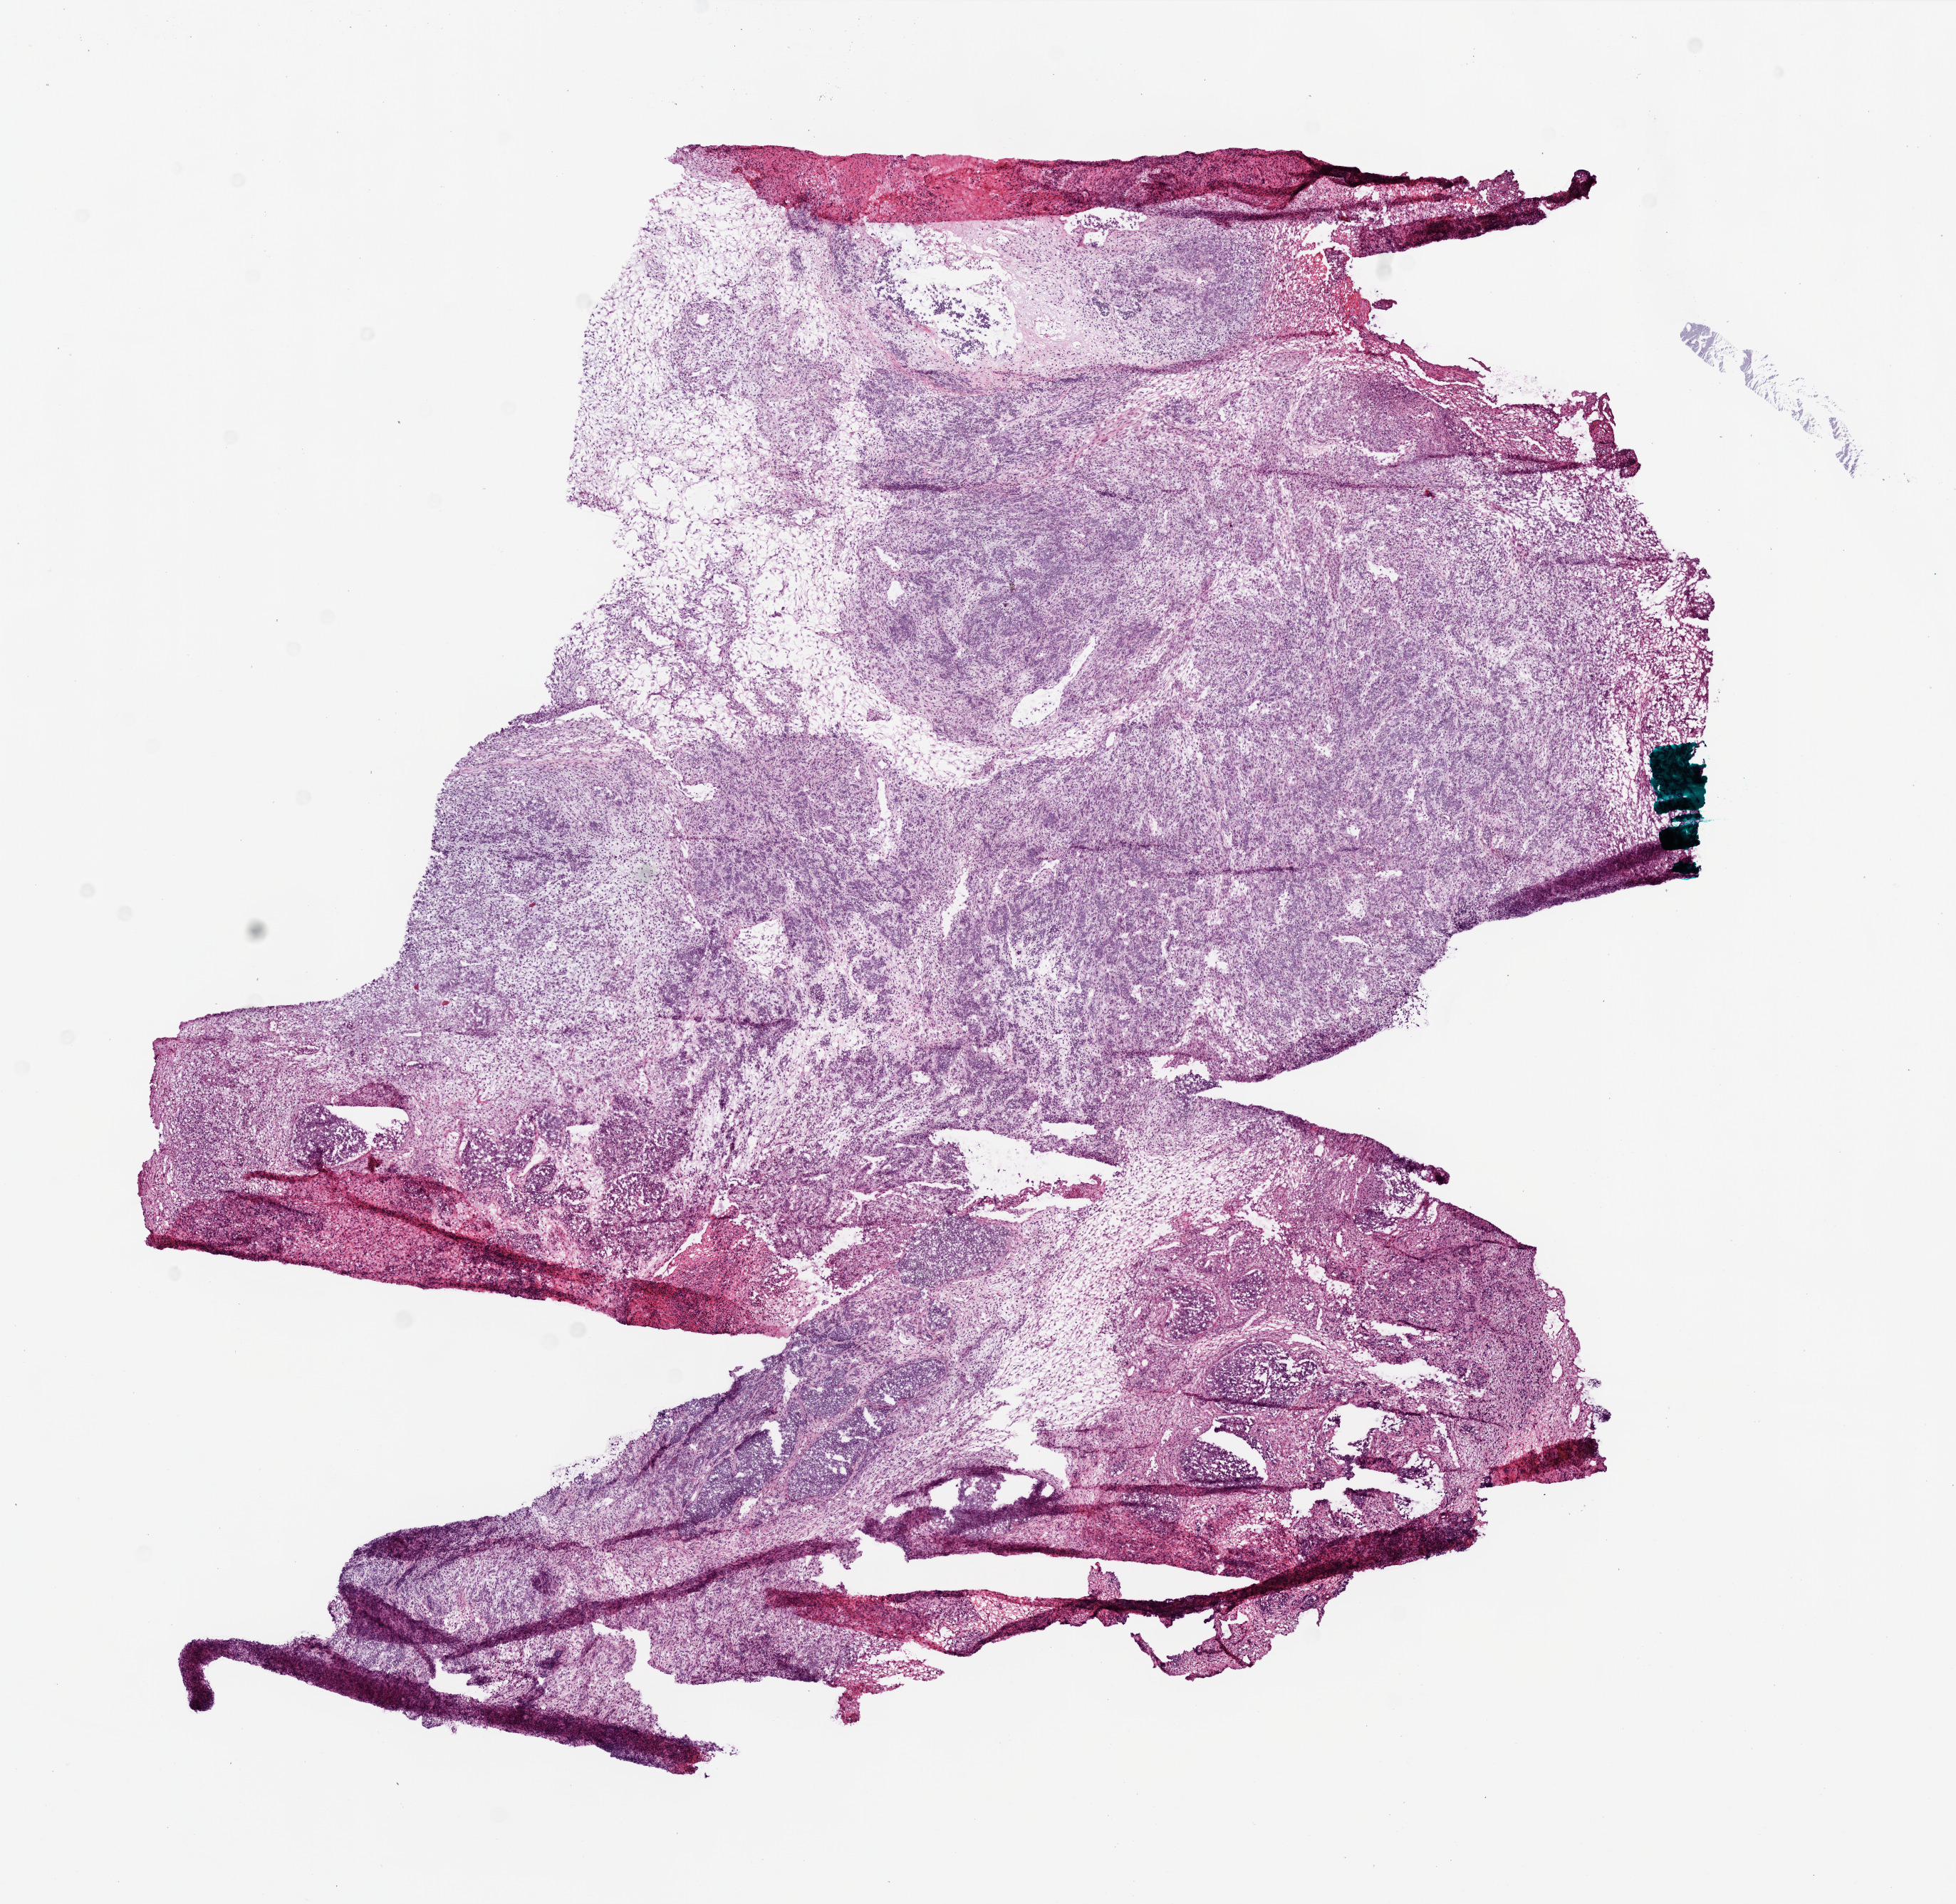
Digitized H&E tissue section (whole slide), whole scanned area (about 11.0 x 10.7 mm, from a 20x scan) shown as a low-resolution overview; frozen section; sample: primary tumour, brain. Male patient; age at initial diagnosis 42 years. Pathologist review of this section (percent, as recorded): tumour cells 75%, tumour nuclei 85%, stromal cells 20%, necrosis 5%.
Histologic diagnosis: Glioblastoma.